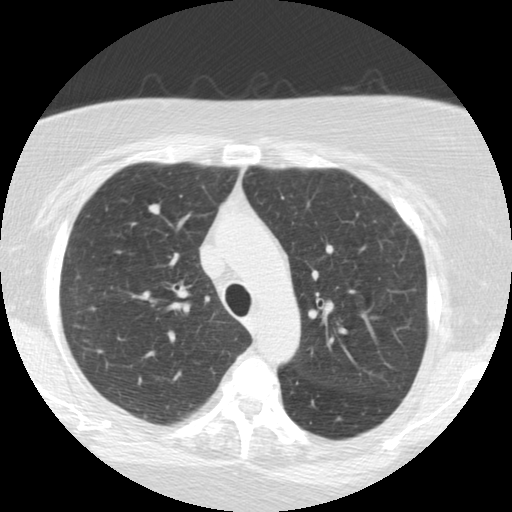
Low-dose screening chest CT, one axial slice; position 169 of 225 along the scan axis; lung window (W 1500 / L -600 HU); 512 × 512 image matrix, field of view 320 × 320 mm.
Structures marked on this image (outlined manually by an expert reader):
- lesion 1 (tumor, upper lobe of right lung): bounding box (x1, y1, x2, y2) in pixels: (149, 204, 160, 215)